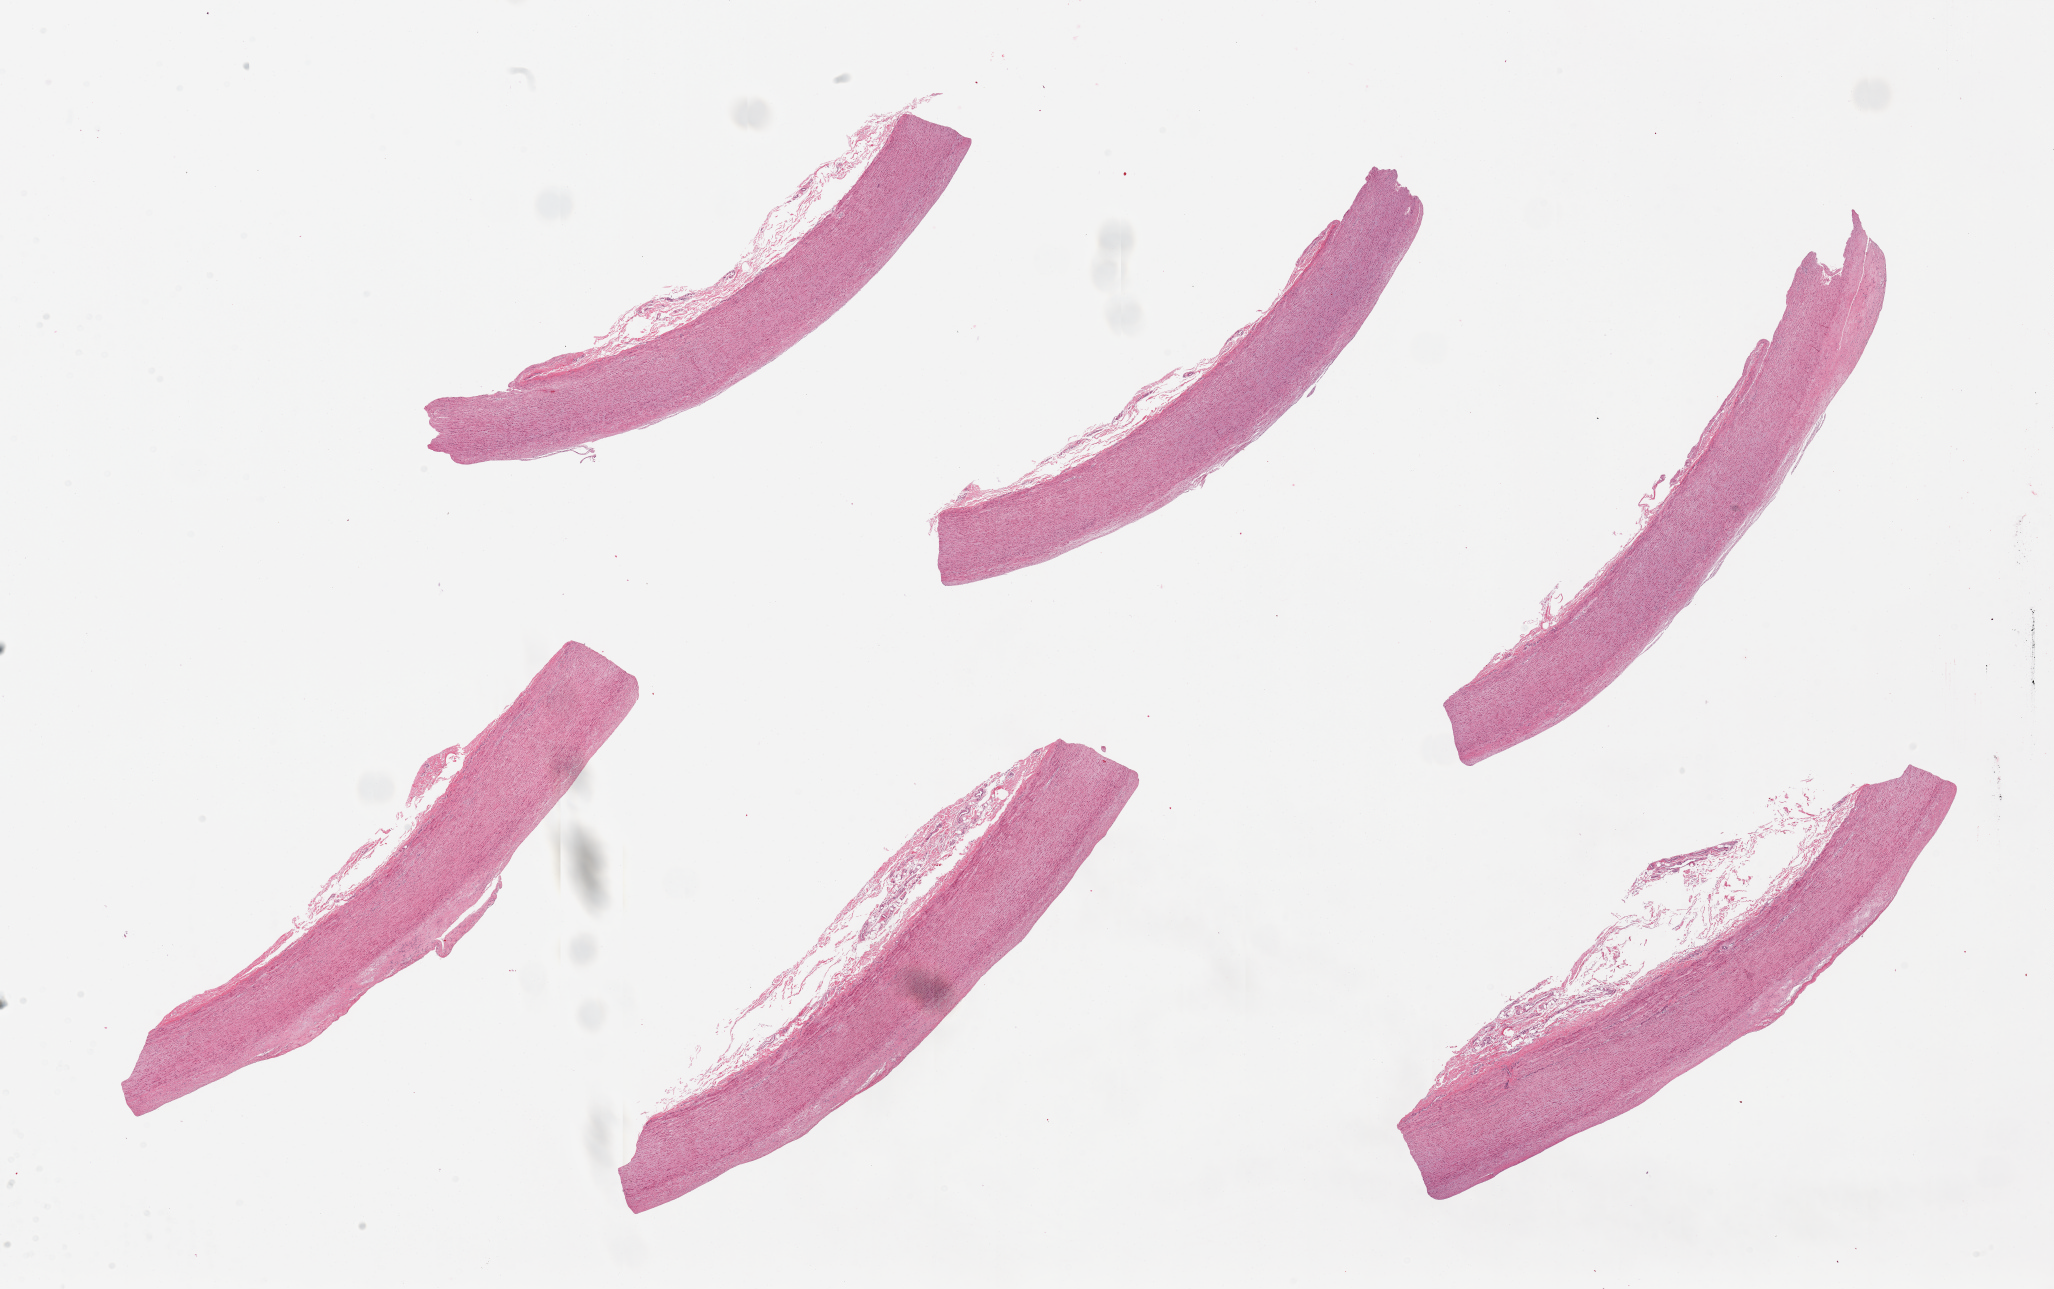
Digitized H&E-stained section — shown as a low-resolution overview of the whole scanned area (about 32.5 x 20.4 mm); PAXgene-fixed paraffin-embedded (PFPE) section; sampled site (target tissue): aorta; donor tissue sample.
Pathologist's review note for this sample: 6 pieces, atheroma with foamy macrophages.